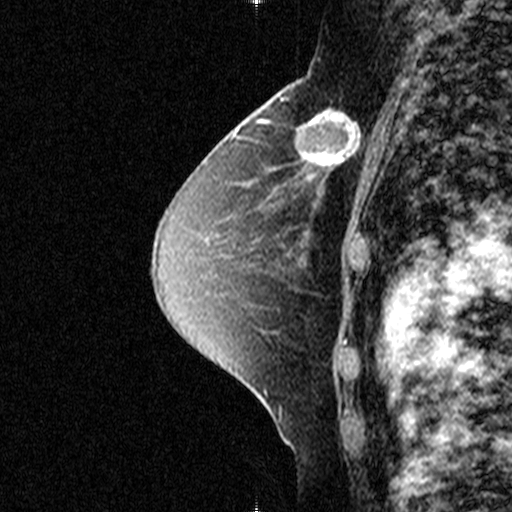
Breast MRI (dynamic contrast-enhanced), one sagittal slice. Position 26 of 44 along the scan axis. Dynamic contrast-enhanced study with each time point stored as its own series, time point 2 of 3 at this slice position (early post-contrast, ordered by acquisition time). 1.5 T. TE 4.5 ms, TR 11 ms. 3 mm slice thickness. 512 × 512 image matrix, field of view 200 × 200 mm. Female patient, age 49 years. From the clinical record (not read from this slice): setting: breast cancer imaged before/during neoadjuvant chemotherapy; receptor status: triple-negative.
Annotated regions visible in this slice (semi-automatically segmented with operator editing):
- analysis volume of interest (the breast-tissue region the enhancement analysis was run in; not a lesion): bounding box (x1, y1, x2, y2) in pixels: (276, 94, 369, 181)
- tumour enhancement mask (voxels above the 90 % enhancement threshold inside the analysis volume of interest): (302, 109, 360, 165)